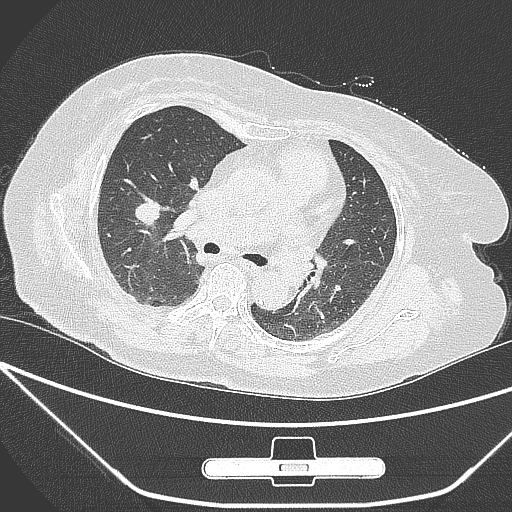
Chest CT, one axial slice; position 159 of 245 along the scan axis; 120 kVp; lung window (W 1500 / L -600 HU); 1 mm slice thickness; 512 × 512 image matrix, field of view 365 × 365 mm. Female patient, age 65 years. Case-level facts recorded for this patient, not image findings: clinical TNM (as recorded): T1c N0 M0; histopathological grade: G3.
Outlined on this slice (rectangle marked by the reading radiologist):
- lung tumour (recorded histology: adenocarcinoma): bounding box [x1, y1, x2, y2] px = [125, 195, 167, 228]